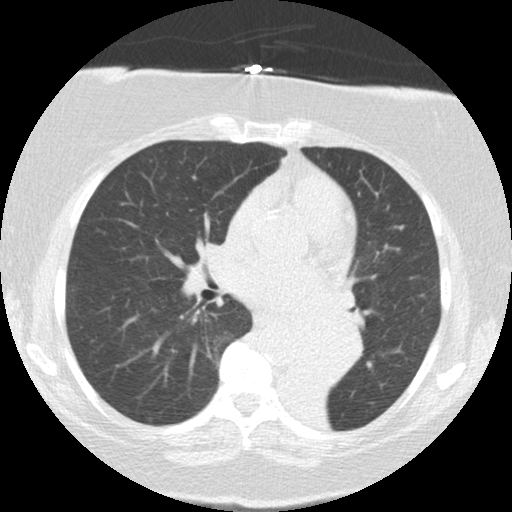
Low-dose screening chest CT, one axial slice. Slice 72 of 136 in the series (ordered by position). Reconstruction kernel STANDARD. 120 kVp. Lung window (W 1500 / L -600 HU). 2.5 mm slice thickness. 512 × 512 image matrix, field of view 309 × 309 mm.
Structures marked on this image (manually delineated by an expert):
- lesion 2 (tumor, mediastinum): bounding box (x1, y1, x2, y2) in pixels: (293, 313, 361, 386)